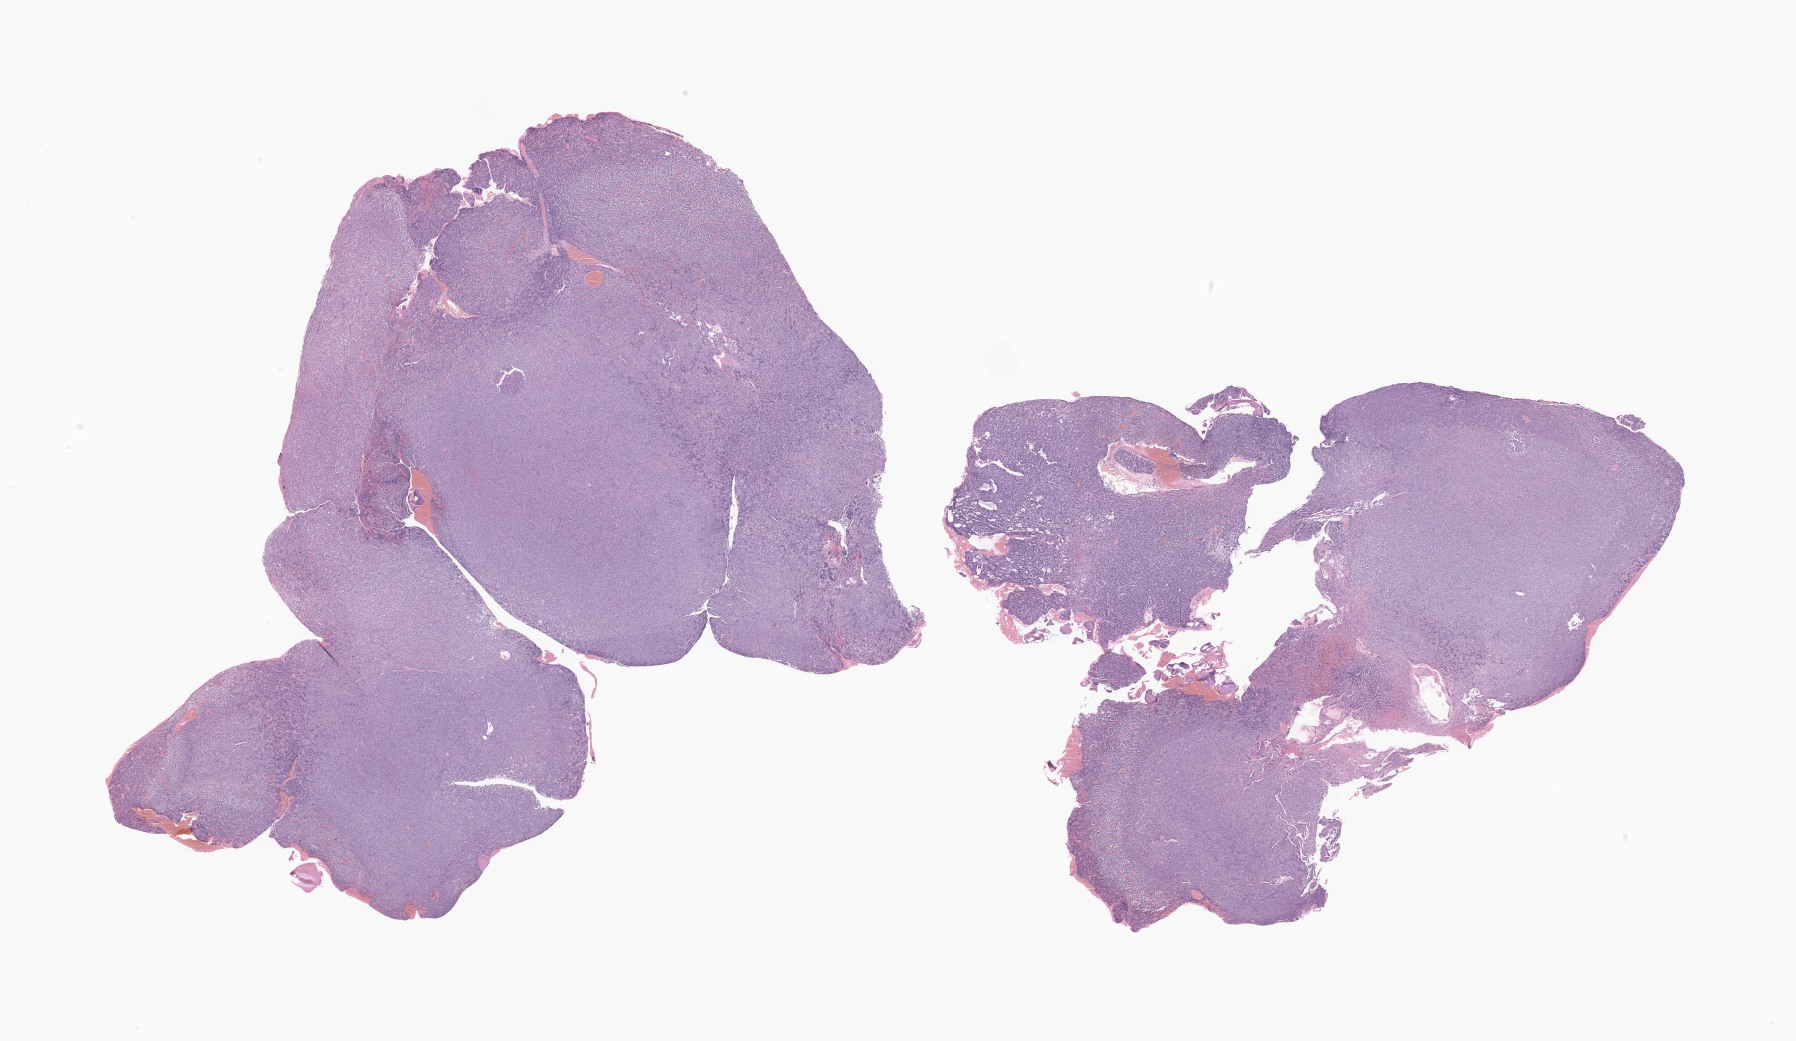
Whole-slide image, H&E stain of tumor tissue from the brain stem, low-resolution overview of the scanned area, about 30.3 x 17.6 mm, formalin-fixed paraffin-embedded section. Patient female; age 43 months (3 years 7 months).
Recorded diagnosis: Ependymoma, NOS.